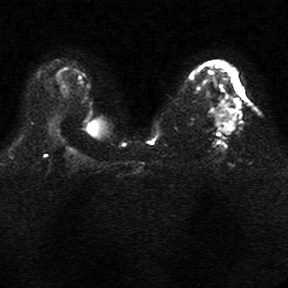
Breast MRI, one axial slice; position 16 of 34 along the scan axis; diffusion-weighted series; image 2 of 4 stored at this slice position (different b-values; order by instance number); 1.5 T; 5 mm slice thickness; 288 × 288 image matrix, field of view 340 × 340 mm. Female patient.
Structures marked on this image (expert manual segmentation):
- tumour on diffusion-weighted imaging: bounding box <222,98,240,132> (left, top, right, bottom; pixels)